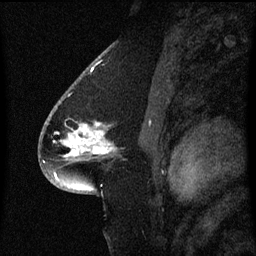
Breast MRI (dynamic contrast-enhanced), one sagittal slice. Slice 38 of 60 in the series (ordered by position). Dynamic contrast-enhanced series, image 2 of 3 at this slice position (ordered by acquisition). 1.5 T. TE 4.2 ms, TR 8.4 ms. 2 mm slice thickness. 256 × 256 image matrix, field of view 200 × 200 mm. Female patient, age 54 years. From the clinical record (not read from this slice): setting: breast cancer imaged before/during neoadjuvant chemotherapy; receptor status: HR-positive, HER2-negative.
Structures marked on this image (semi-automatic segmentation, software-assisted and operator-edited):
- analysis volume of interest (the breast-tissue region the enhancement analysis was run in; not a lesion): bounding box [x1, y1, x2, y2] px = [46, 104, 115, 171]
- tumour enhancement mask (voxels above the 70 % enhancement threshold inside the analysis volume of interest): [66, 124, 111, 157]